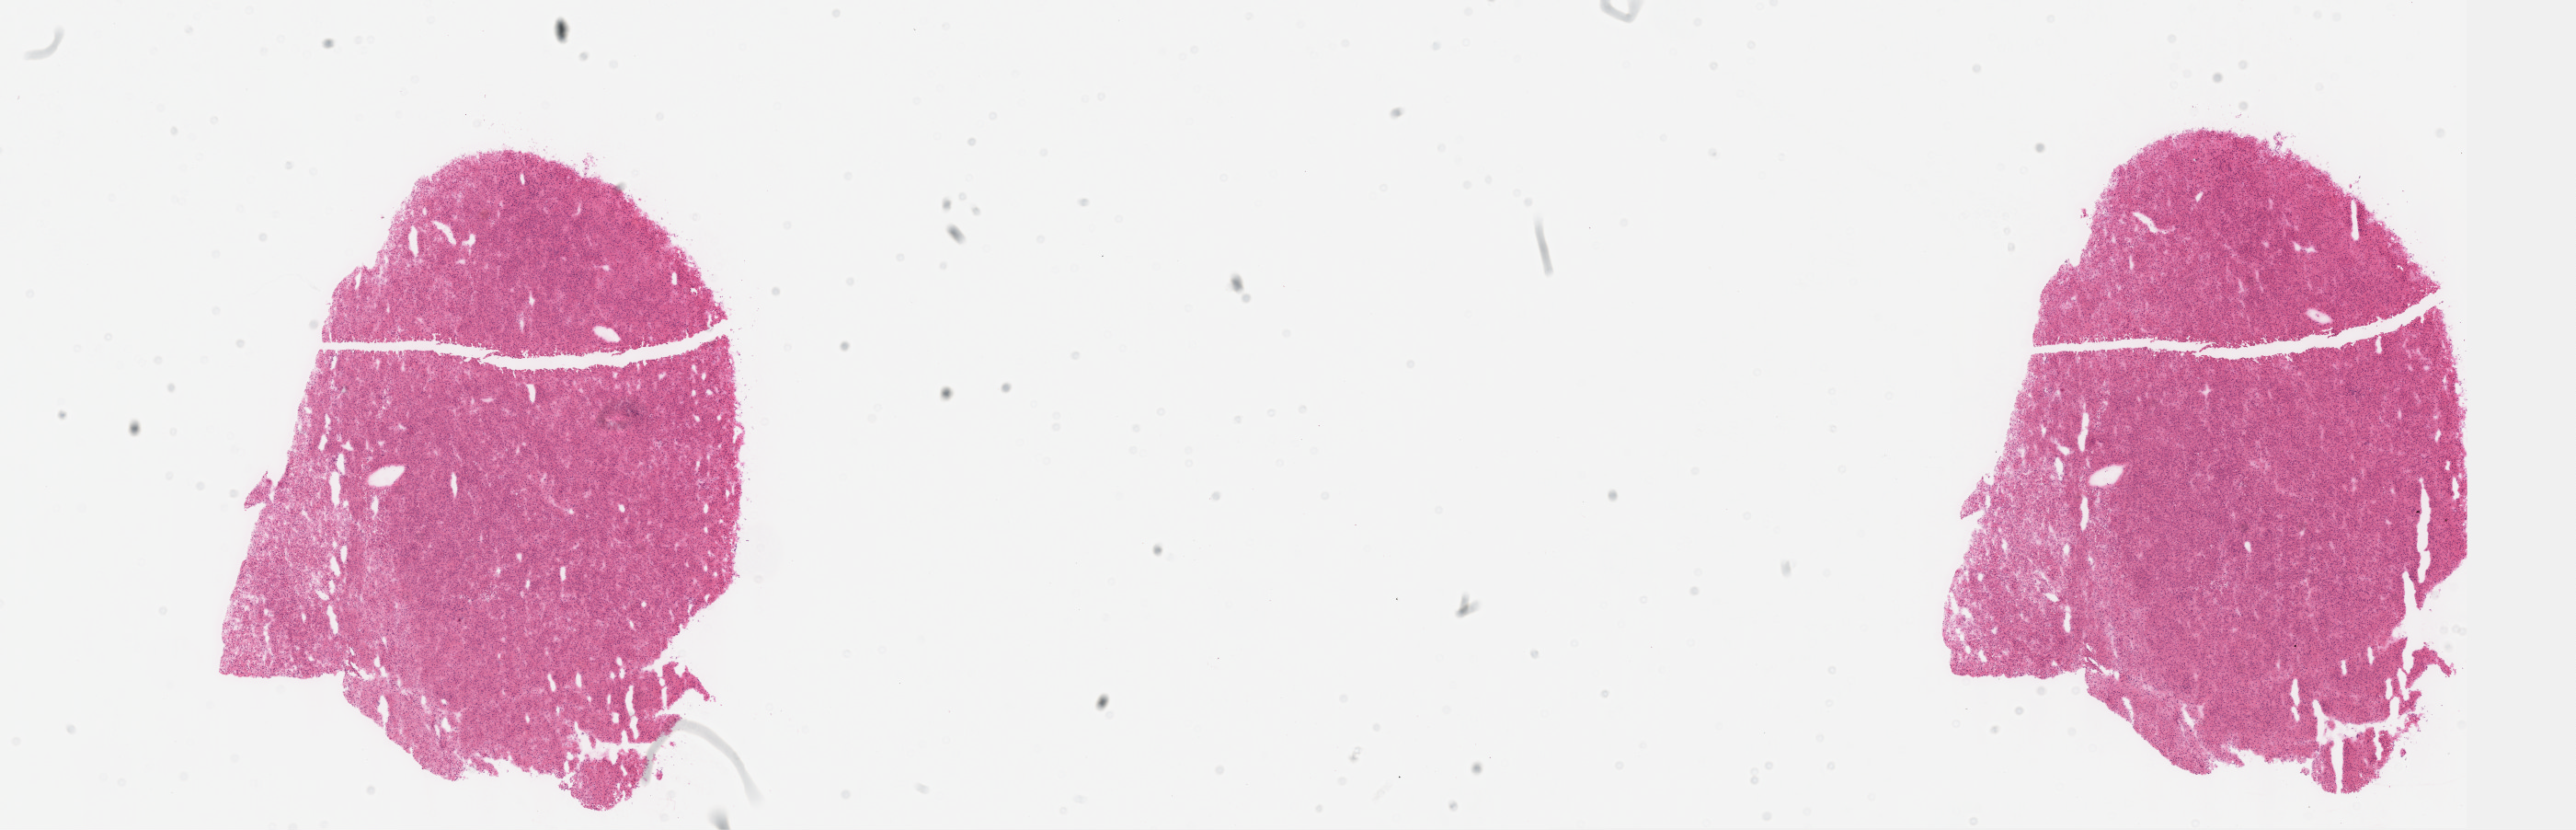
Hematoxylin and eosin (H&E) stained whole-slide image — whole scanned area (about 22.6 x 7.3 mm, from a 40x scan) shown as a low-resolution overview. Frozen section from the top of the tissue portion. Kidney, primary tumour sample. Female, age 45 years at initial diagnosis. Slide review estimates, as recorded: tumour cells 85%, tumour nuclei 85%, normal cells 0%, stromal cells 15%, necrosis 0%. Inflammatory infiltration, as recorded: lymphocyte infiltration 2%, monocyte infiltration 1%, neutrophil infiltration 1%.
Histologic diagnosis: Renal cell carcinoma, chromophobe type. AJCC pathologic stage: I (6th edition). Laterality: left. TNM: T1a NX.